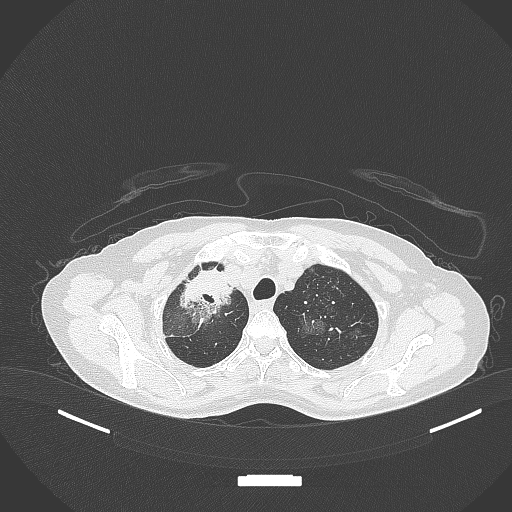
Chest CT, one axial slice; position 273 of 284 along the scan axis; reconstruction kernel B70f; 120 kVp; lung window (W 1500 / L -600 HU); 1 mm slice thickness; 512 × 512 image matrix, field of view 400 × 400 mm. Female patient, age 59 years. From the clinical record (not read from this slice): clinical TNM (as recorded): T3 N0 M0.
Structures marked on this image (bounding box drawn by a radiologist):
- lung tumour (recorded histology: adenocarcinoma): bounding box (x1, y1, x2, y2) in pixels: (177, 266, 236, 325)